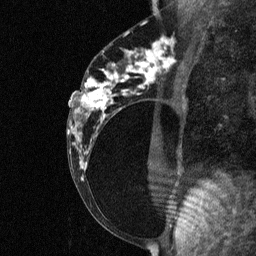
Breast MRI (dynamic contrast-enhanced), one sagittal slice. Slice 33 of 64 in the series (ordered by position). Dynamic contrast-enhanced study with each time point stored as its own series, time point 2 of 3 at this slice position (early post-contrast, ordered by acquisition time). 1.5 T. TE 4.8 ms, TR 27 ms. 2 mm slice thickness. 256 × 256 image matrix. Female patient, age 34 years. Case-level facts recorded for this patient, not image findings: setting: breast cancer imaged before/during neoadjuvant chemotherapy; receptor status: HR-positive, HER2-negative.
Annotated regions visible in this slice (semi-automatically segmented with operator editing):
- analysis volume of interest (the breast-tissue region the enhancement analysis was run in; not a lesion): bounding box [x1, y1, x2, y2] px = [78, 44, 181, 191]
- tumour enhancement mask (voxels above the 90 % enhancement threshold inside the analysis volume of interest): [81, 51, 165, 167]